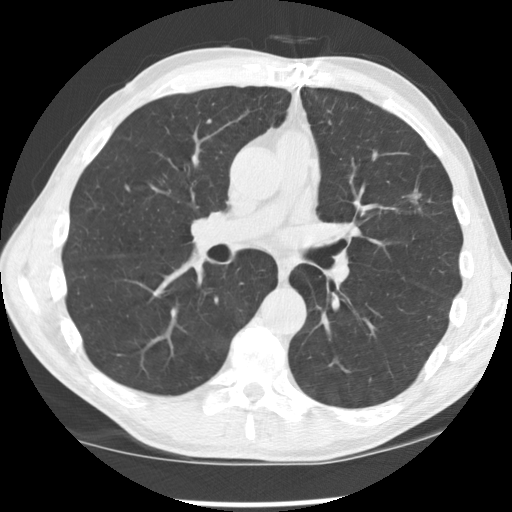
Low-dose screening chest CT, axial slice; second annual screen; lung window (W 1500 / L -600 HU); 2.5 mm slice thickness; standard (soft-tissue) reconstruction kernel (STANDARD); 120 kVp; 512 × 512 image matrix. Male participant, aged 64 years at enrolment. Current smoker at enrolment.
- Expert-annotated lung lesion, bounding box <384,175,440,223> (left, top, right, bottom; pixels).
- The exam's reader record, not a measurement of the box and not confirmed to be the same lesion: non-calcified nodule or mass ≥4 mm, left upper lobe, 16 × 11 mm, spiculated (stellate) margins, soft tissue attenuation, pre-existing on the prior screen: yes; interval growth: yes.
- Official screen result: positive, other.